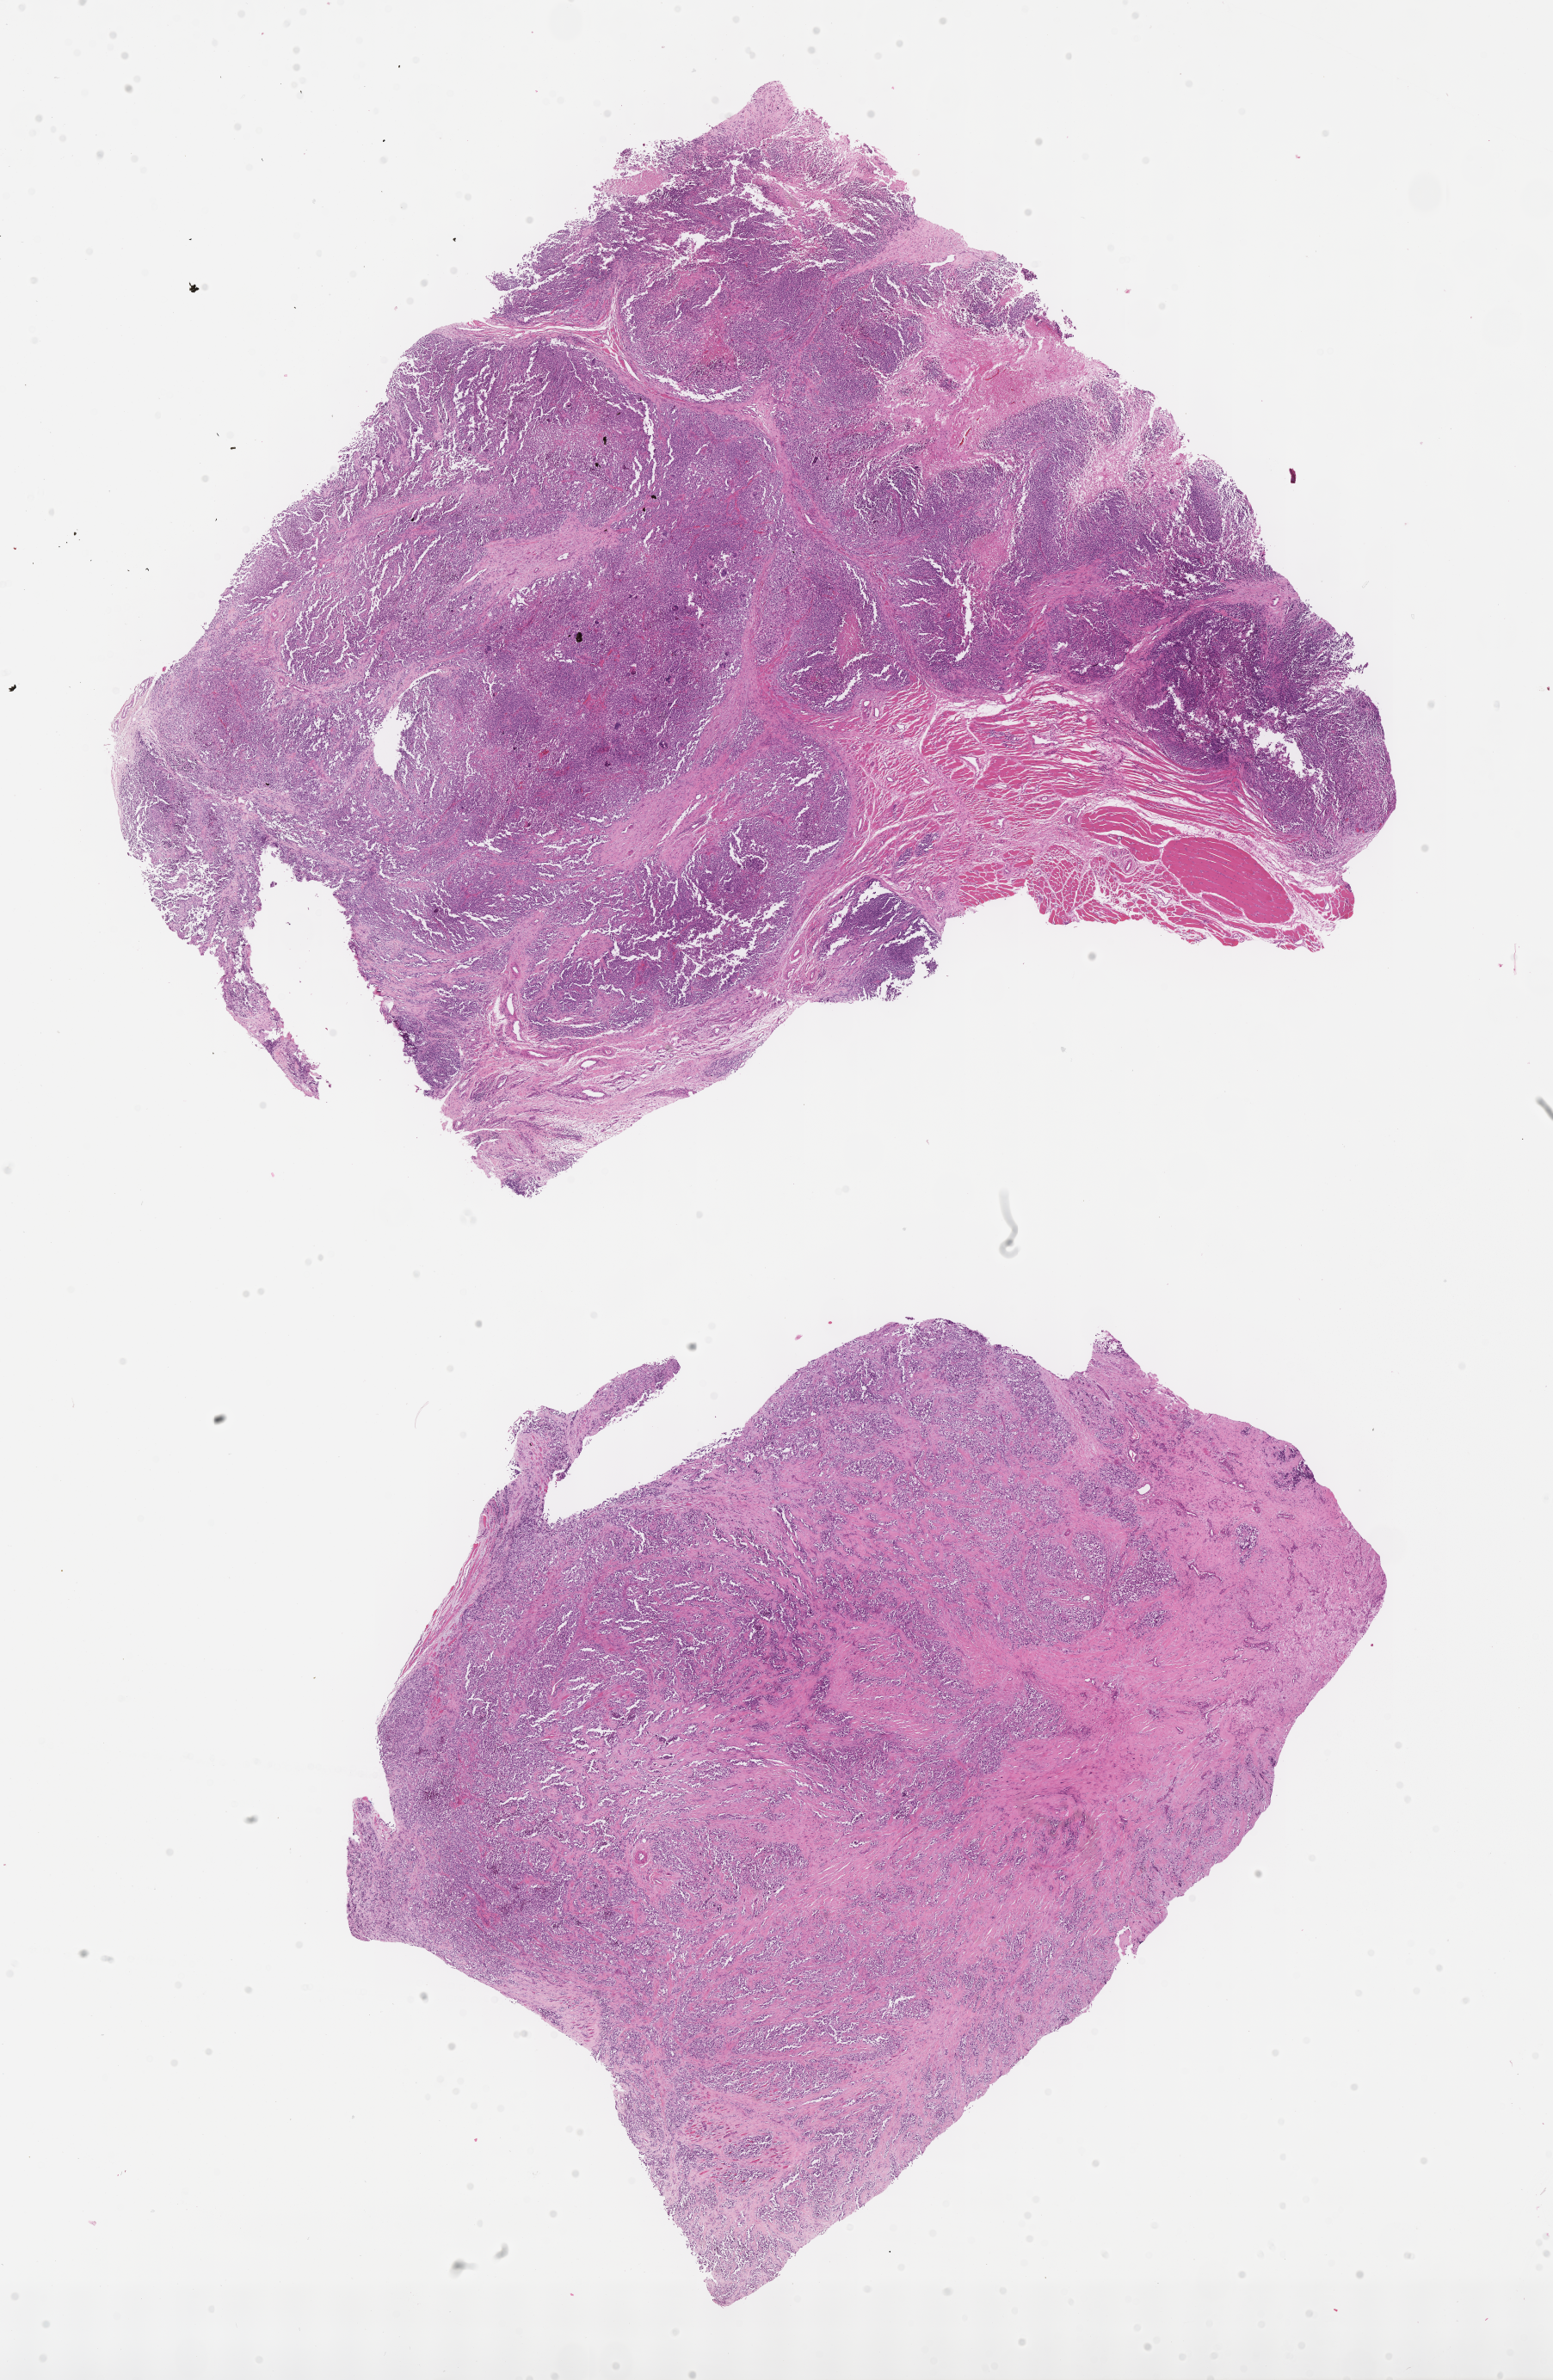
Digitized hematoxylin and eosin (H&E)-stained section of tumor tissue, whole scanned area (about 14.6 x 22.4 mm) shown as a low-resolution overview; formalin-fixed, paraffin-embedded (FFPE) tissue; sample anatomic site: soft tissue - hand, right. Female patient, age at diagnosis 14.0 years.
Diagnosis: rhabdomyosarcoma; histological classification: alveolar rhabdomyosarcoma.